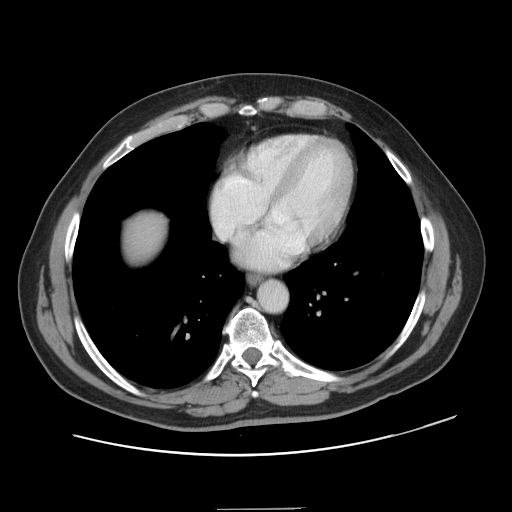
Contrast-enhanced abdominal CT, one axial slice. Position 143 of 143 along the scan axis. 120 kVp. Intravenous contrast given. Soft-tissue window (W 400 / L 40 HU). 512 × 512 image matrix, field of view 402 × 402 mm. Male patient, age 62 years. From the clinical record (not read from this slice): diagnosis: colorectal cancer liver metastases, imaged before liver resection; multiple liver metastases: yes; largest metastasis: 2.7 cm; disease in both lobes: no.
Structures marked on this image (manually delineated by an expert):
- liver: box from (x=125, y=216) to (x=163, y=263) px
- planned liver remnant (the part of the liver to remain after resection): (x=125, y=216)–(x=163, y=264)